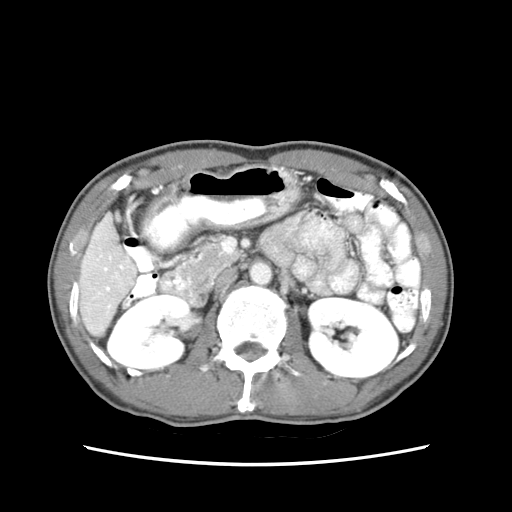
Contrast-enhanced abdominal CT (liver protocol), one axial slice. Slice 22 of 79 in the series (ordered by position). Reconstruction kernel STANDARD. 120 kVp. Soft-tissue window (W 400 / L 40 HU). 2.5 mm slice thickness. 512 × 512 image matrix. From the clinical record (not read from this slice): diagnosis: hepatocellular carcinoma (patient treated with transarterial chemoembolisation; whether this scan precedes or follows treatment is not stated here); TNM stage (as recorded): Stage-IIIB; Child-Pugh class: A; tumour differentiation: moderately differentiated; tumour nodularity: multinodular.
Outlined on this slice (semi-automatic segmentation, software-assisted and operator-edited):
- liver parenchyma outside the tumour (the mass and vessels are separate outlines, so this box may not span the whole liver): bounding box <78,210,136,336> (left, top, right, bottom; pixels)
- liver vessels: <84,212,131,321>